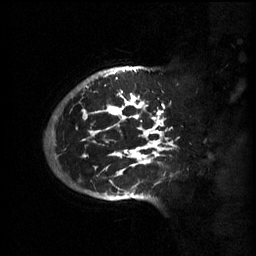
Breast MRI (dynamic contrast-enhanced), one sagittal slice; position 48 of 60 along the scan axis; 3 images stored at this slice position (order not interpretable as contrast timing); 1.5 T; TE 4.2 ms, TR 11 ms; 2 mm slice thickness; 256 × 256 image matrix. Patient: female, 51 years.
Structures marked on this image (semi-automatically segmented with operator editing):
- analysis volume of interest (the breast-tissue region the enhancement analysis was run in; not a lesion): bounding box <63,80,180,201> (left, top, right, bottom; pixels)
- tumour enhancement mask (voxels above the 70 % enhancement threshold inside the analysis volume of interest): <82,86,175,197>